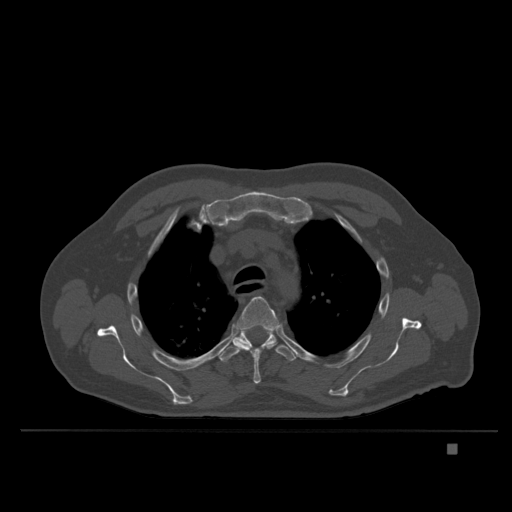
CT including the spine, one axial slice. Position 282 of 435 along the scan axis. Bone window (W 1800 / L 400 HU). 1.5 mm slice thickness. 512 × 512 image matrix. Male patient, age 73 years. From the clinical record (not read from this slice): primary cancer: skin.
Annotated regions visible in this slice (semi-automatically segmented with operator editing):
- T4 vertebra: box from (x=233, y=296) to (x=279, y=384) px
- T5 vertebra: (x=220, y=331)–(x=296, y=363)